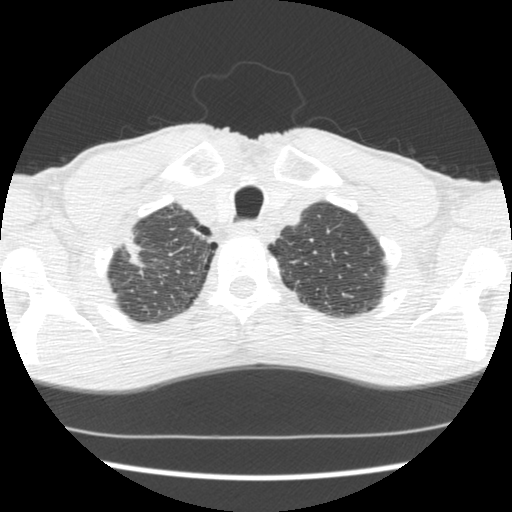
Axial slice from a low-dose chest CT screening exam; baseline screening round; lung window (W 1500 / L -600 HU); 2.5 mm slice thickness; standard (soft-tissue) reconstruction kernel (STANDARD); 120 kVp; 512 × 512 image matrix, field of view 318 × 318 mm. Male, age 62 years at enrolment. Current smoker at enrolment.
Expert-annotated lung lesion, box from (x=102, y=226) to (x=152, y=273) px. No non-calcified nodule or mass ≥4 mm was recorded by the screening reader at this exam. Later outcome: lung cancer diagnosed 640 days after this screen — adenocarcinoma, NOS, right upper lobe, poorly differentiated (G3), stage IIA (AJCC 6th edition), 22 mm at pathology.